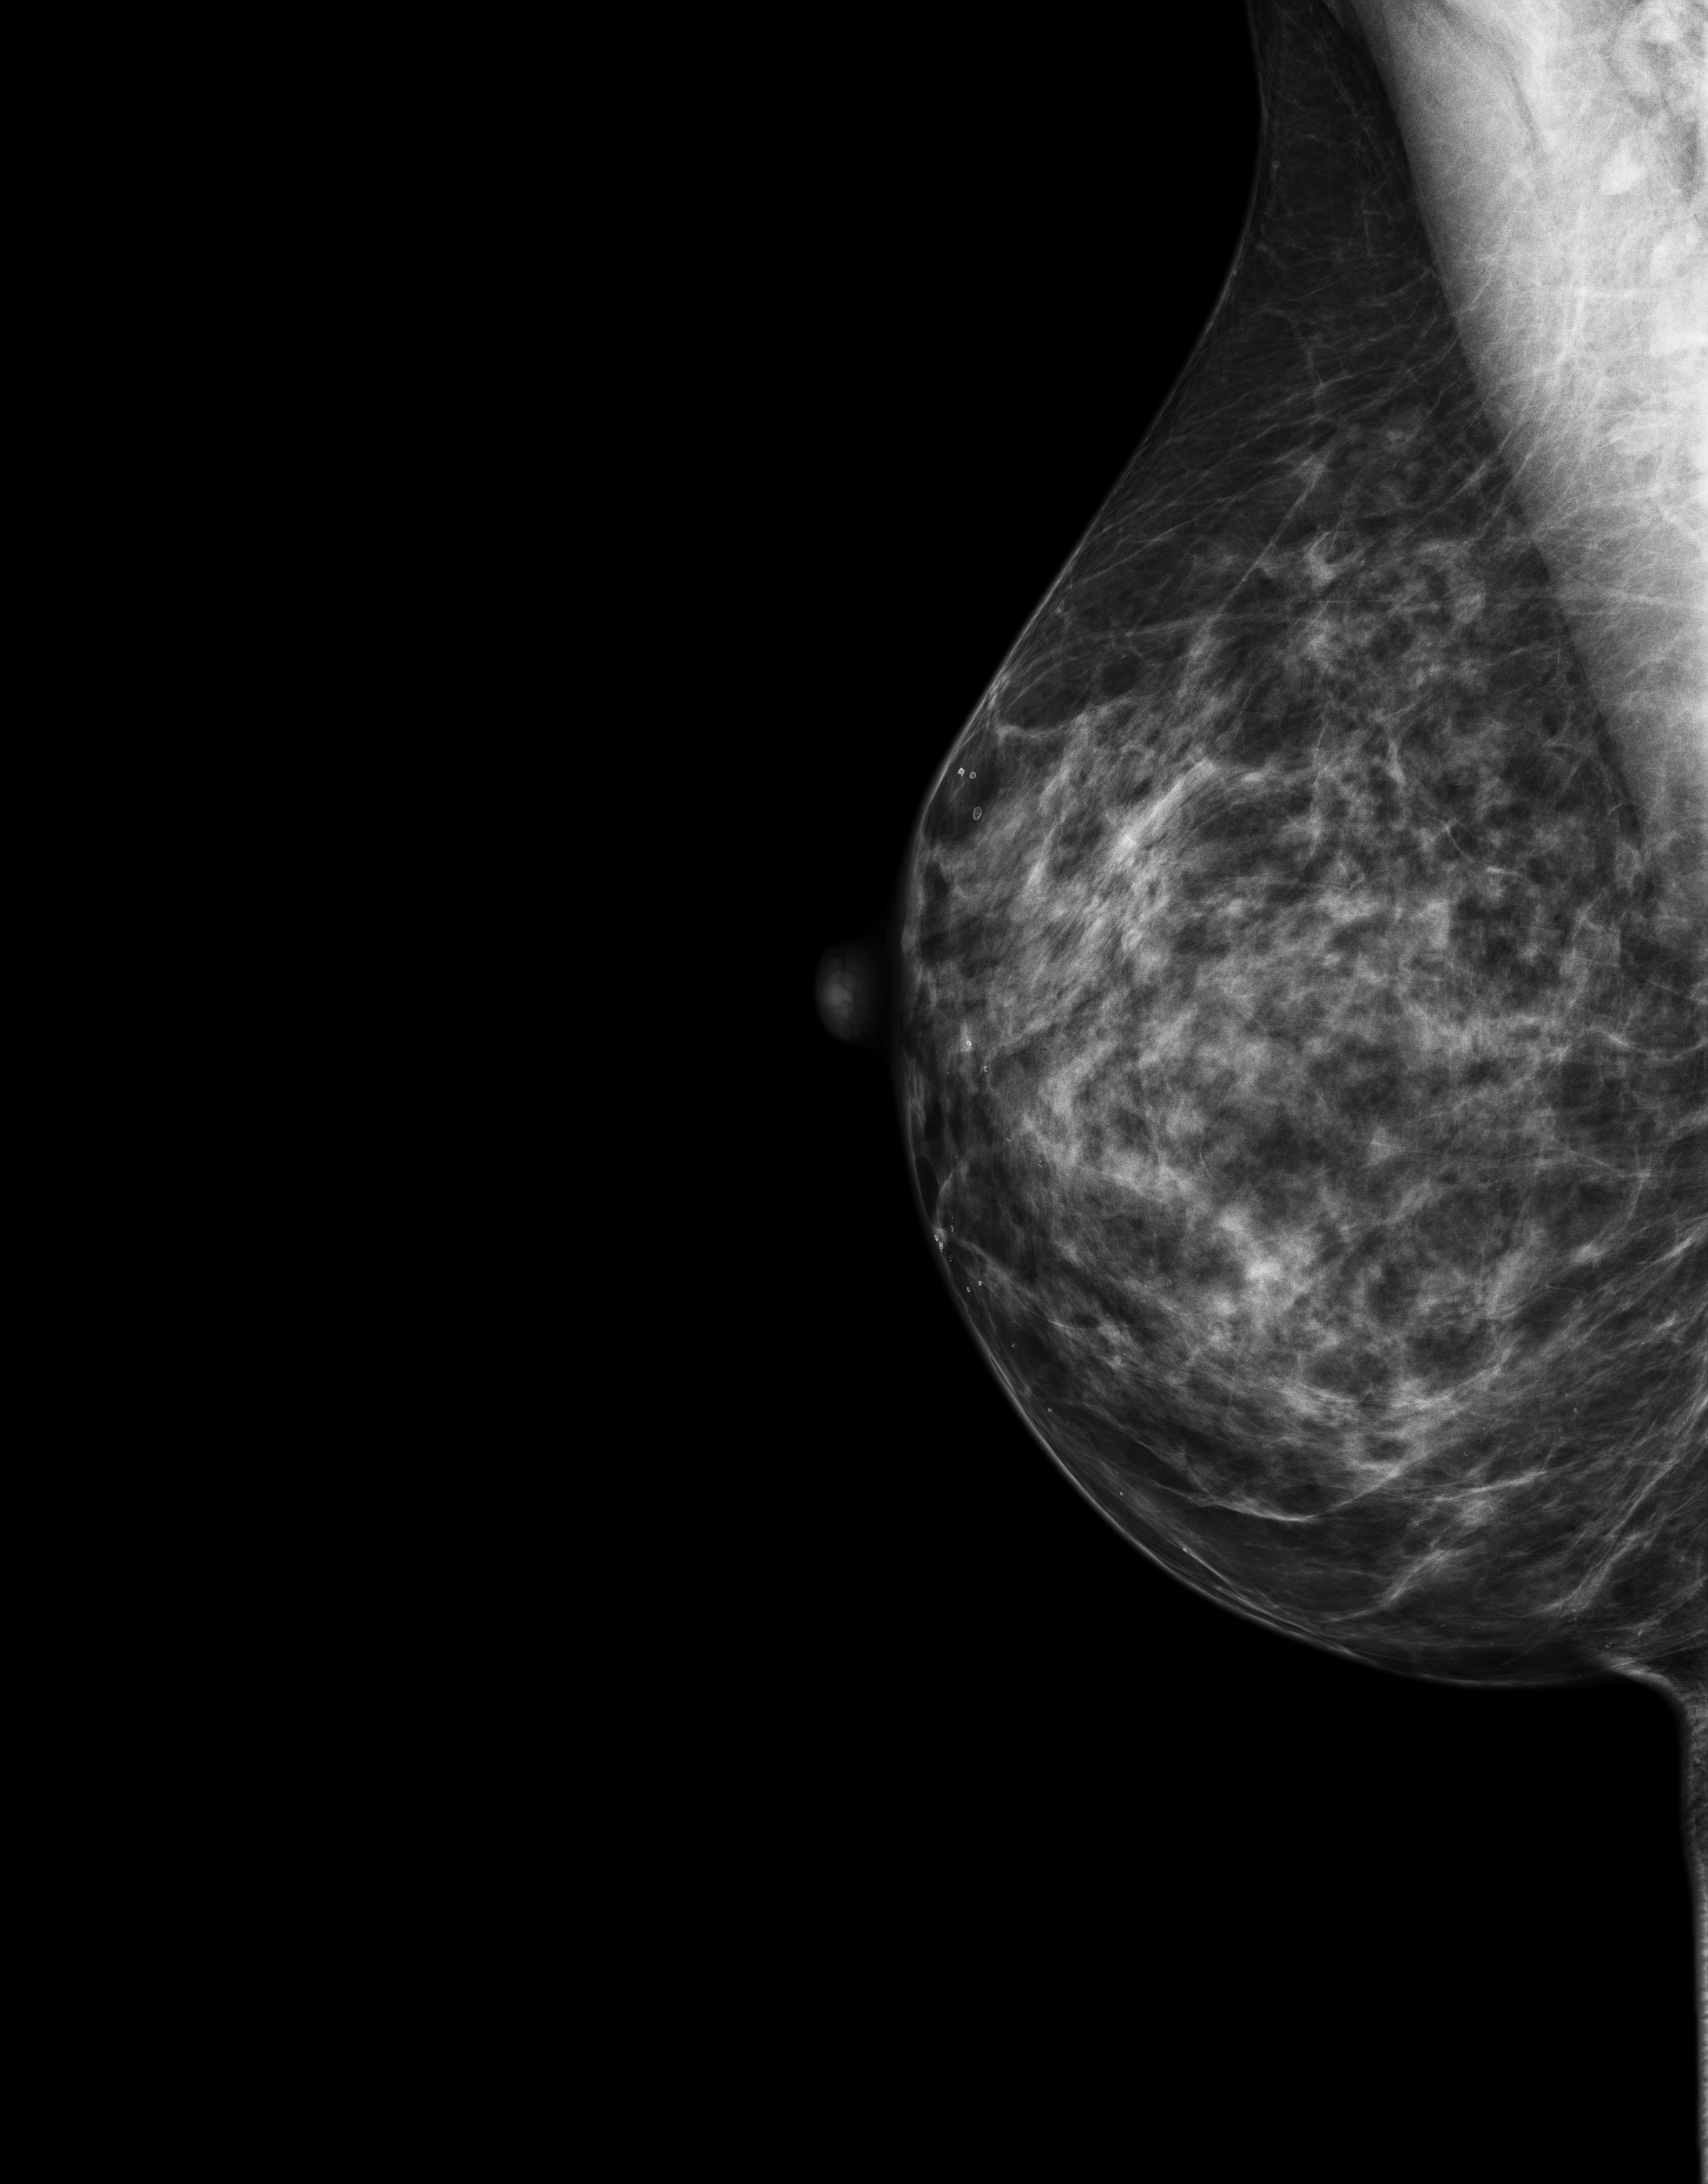
Digital mammogram (FFDM); right breast; MLO view; screening examination. Patient: female, 46 years.
Breast density at the screening exam (both breasts): heterogeneously dense (BI-RADS density category c). Final BI-RADS category for the screening round (tomosynthesis exam, both breasts): category 2. Recall: no recall after this screen.